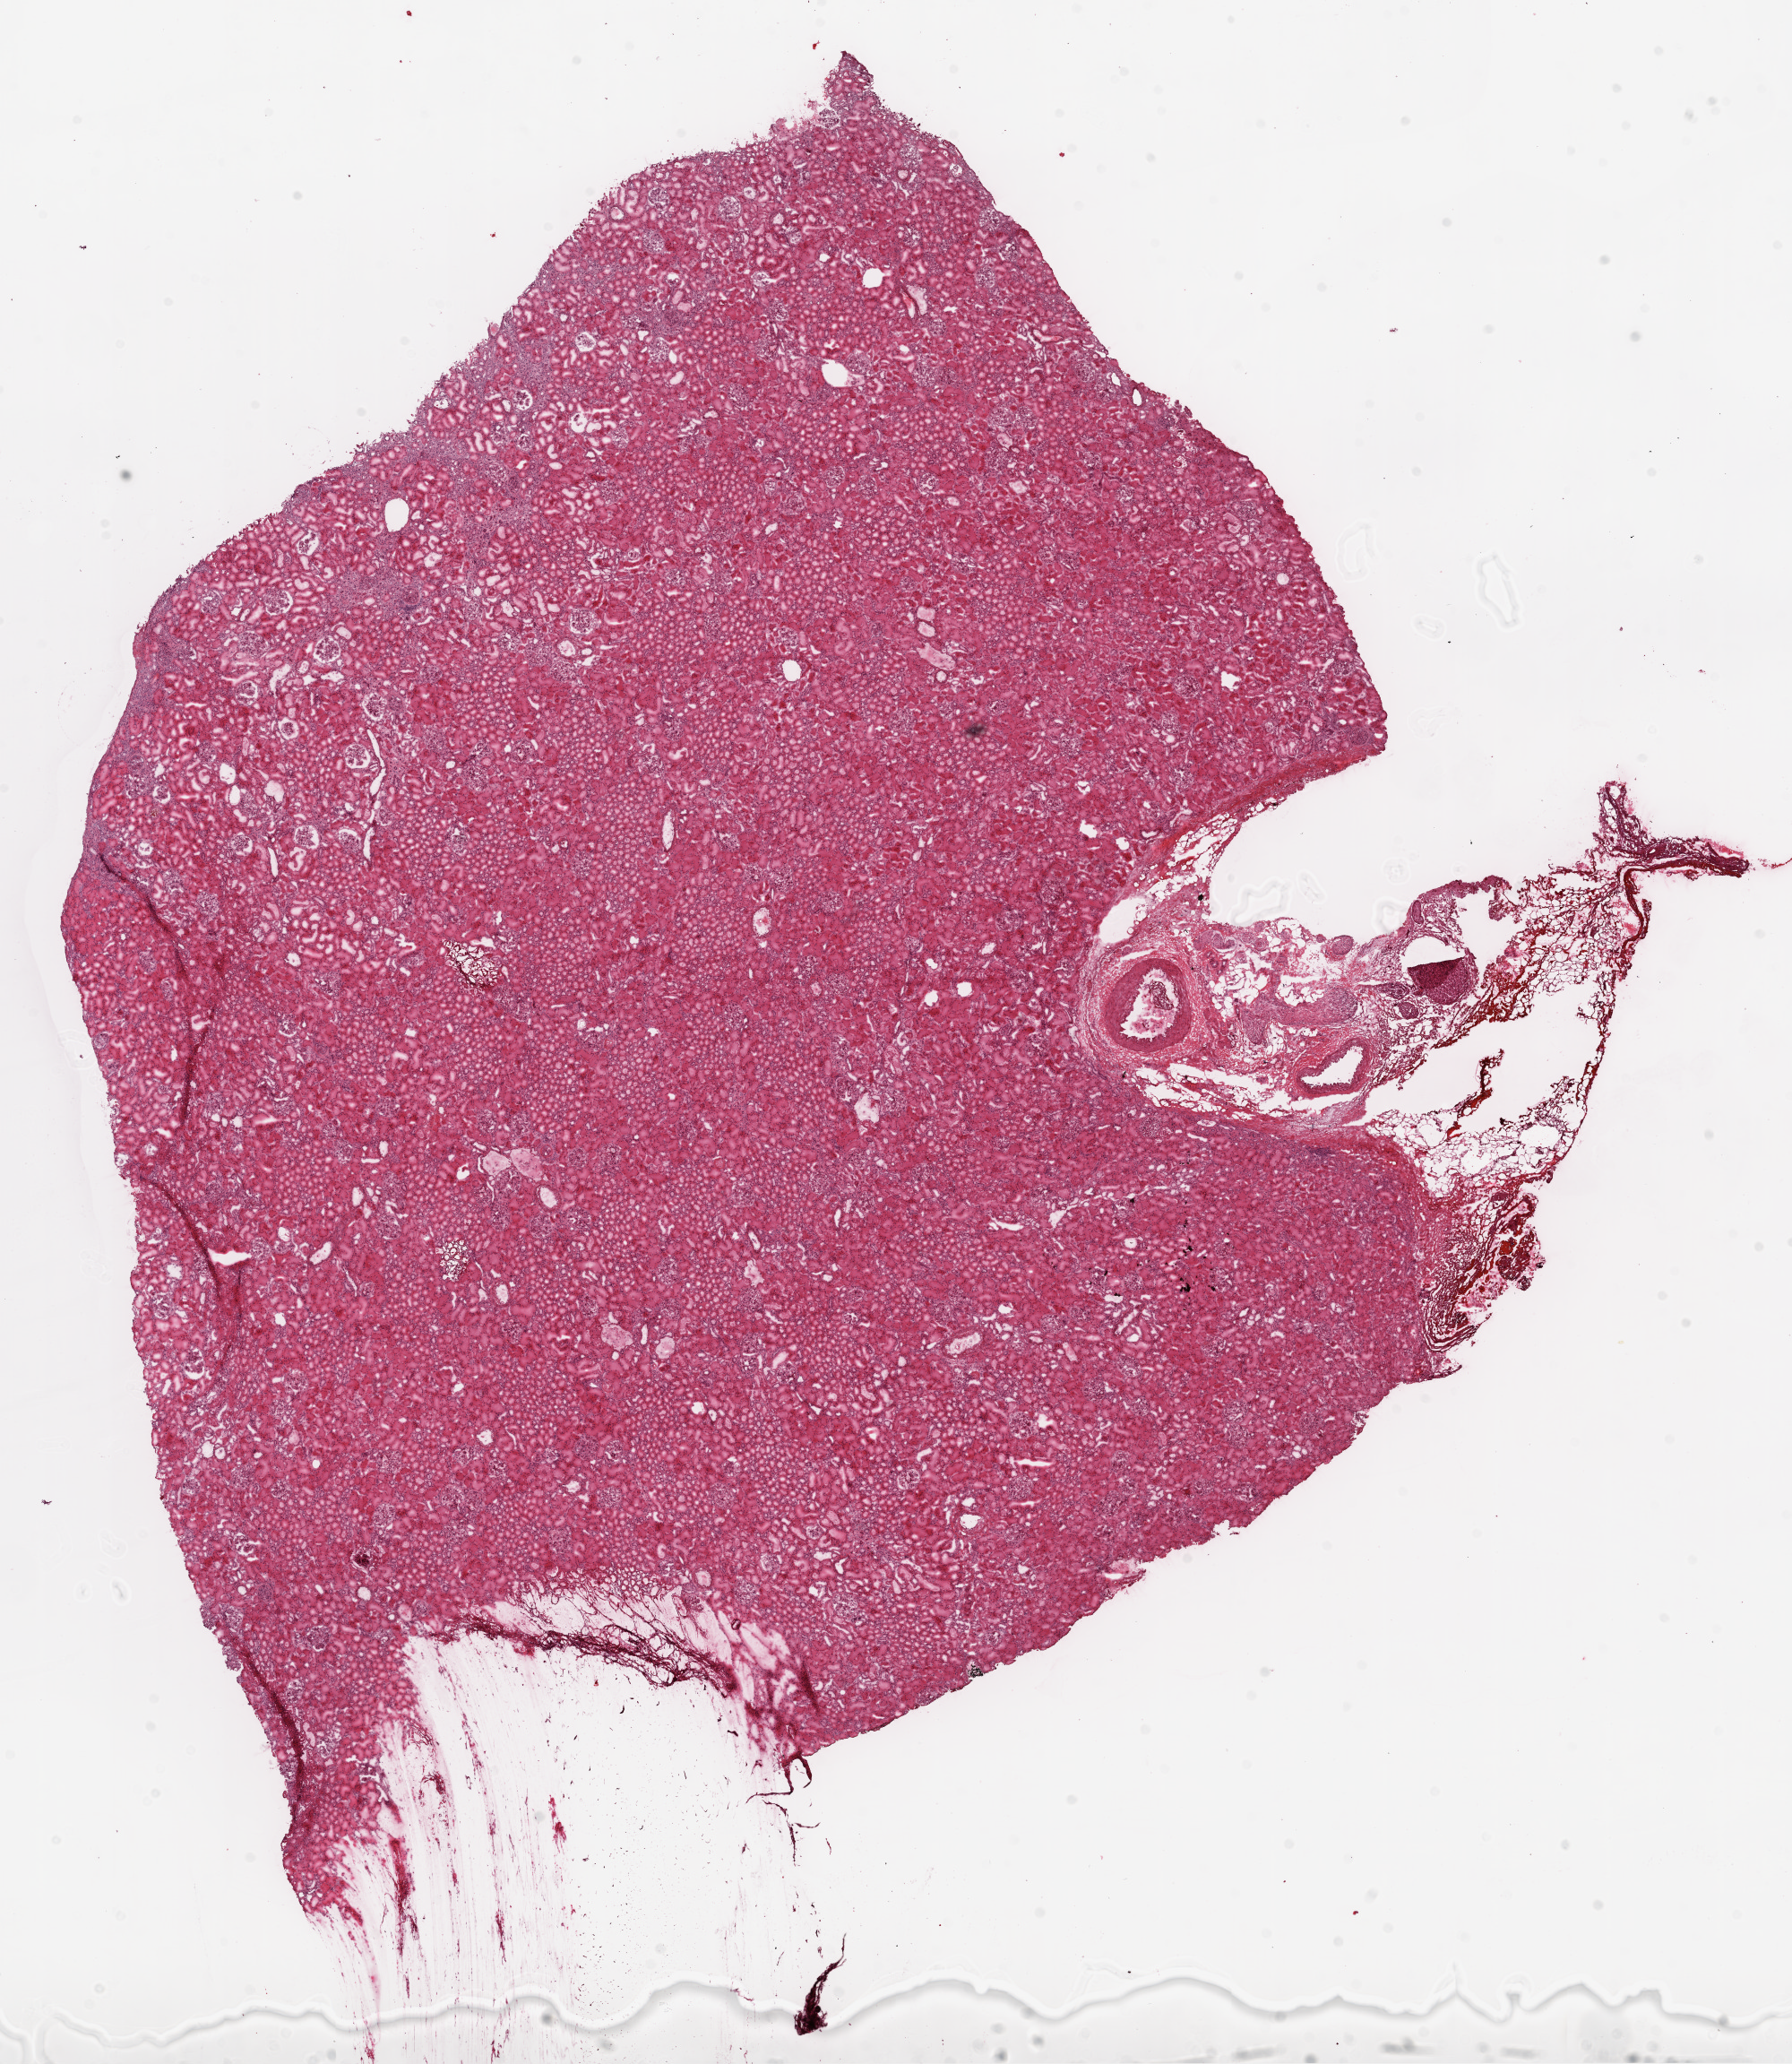
Hematoxylin and eosin (H&E) stained whole-slide image — shown as a low-resolution overview of the whole scanned area (about 16.0 x 18.5 mm, slide scanned at 20x), frozen section from the top of the tissue portion, solid tissue normal (non-tumour tissue) sample from the kidney. Male patient; age at initial diagnosis 44 years.
This section: solid tissue normal sample (biorepository sample class). Patient diagnosis: Clear cell adenocarcinoma, NOS.